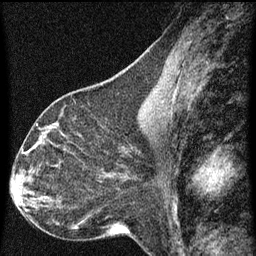
Breast MRI (dynamic contrast-enhanced), one sagittal slice. Slice 32 of 60 in the series (ordered by position). Dynamic contrast-enhanced series, image 2 of 3 at this slice position (ordered by acquisition). 1.5 T. TE 4.2 ms, TR 8 ms. 2 mm slice thickness. 256 × 256 image matrix. Patient: female, 44 years.
Structures marked on this image (semi-automatic segmentation, software-assisted and operator-edited):
- analysis volume of interest (the breast-tissue region the enhancement analysis was run in; not a lesion): bounding box [x1, y1, x2, y2] px = [49, 128, 95, 169]
- tumour enhancement mask (voxels above the 70 % enhancement threshold inside the analysis volume of interest): [49, 128, 66, 137]